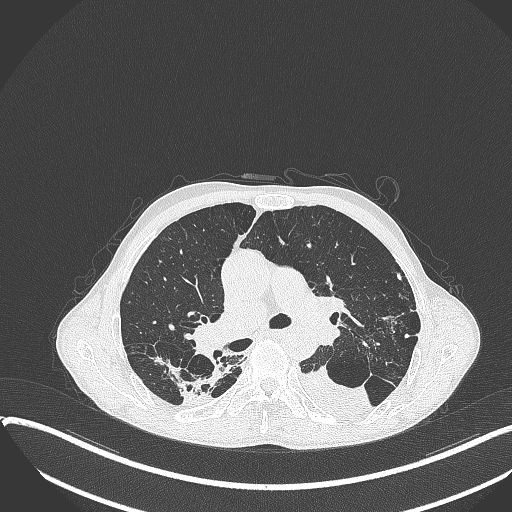
Chest CT, one axial slice; position 237 of 401 along the scan axis; 120 kVp; lung window (W 1500 / L -600 HU); 1 mm slice thickness; 512 × 512 image matrix, field of view 400 × 400 mm. Patient: male, 57 years. Case-level facts recorded for this patient, not image findings: clinical TNM (as recorded): T4 N0 M0.
Annotated regions visible in this slice (rectangle marked by the reading radiologist):
- lung tumour (recorded histology: squamous cell carcinoma): bounding box (x1, y1, x2, y2) in pixels: (298, 361, 374, 424)